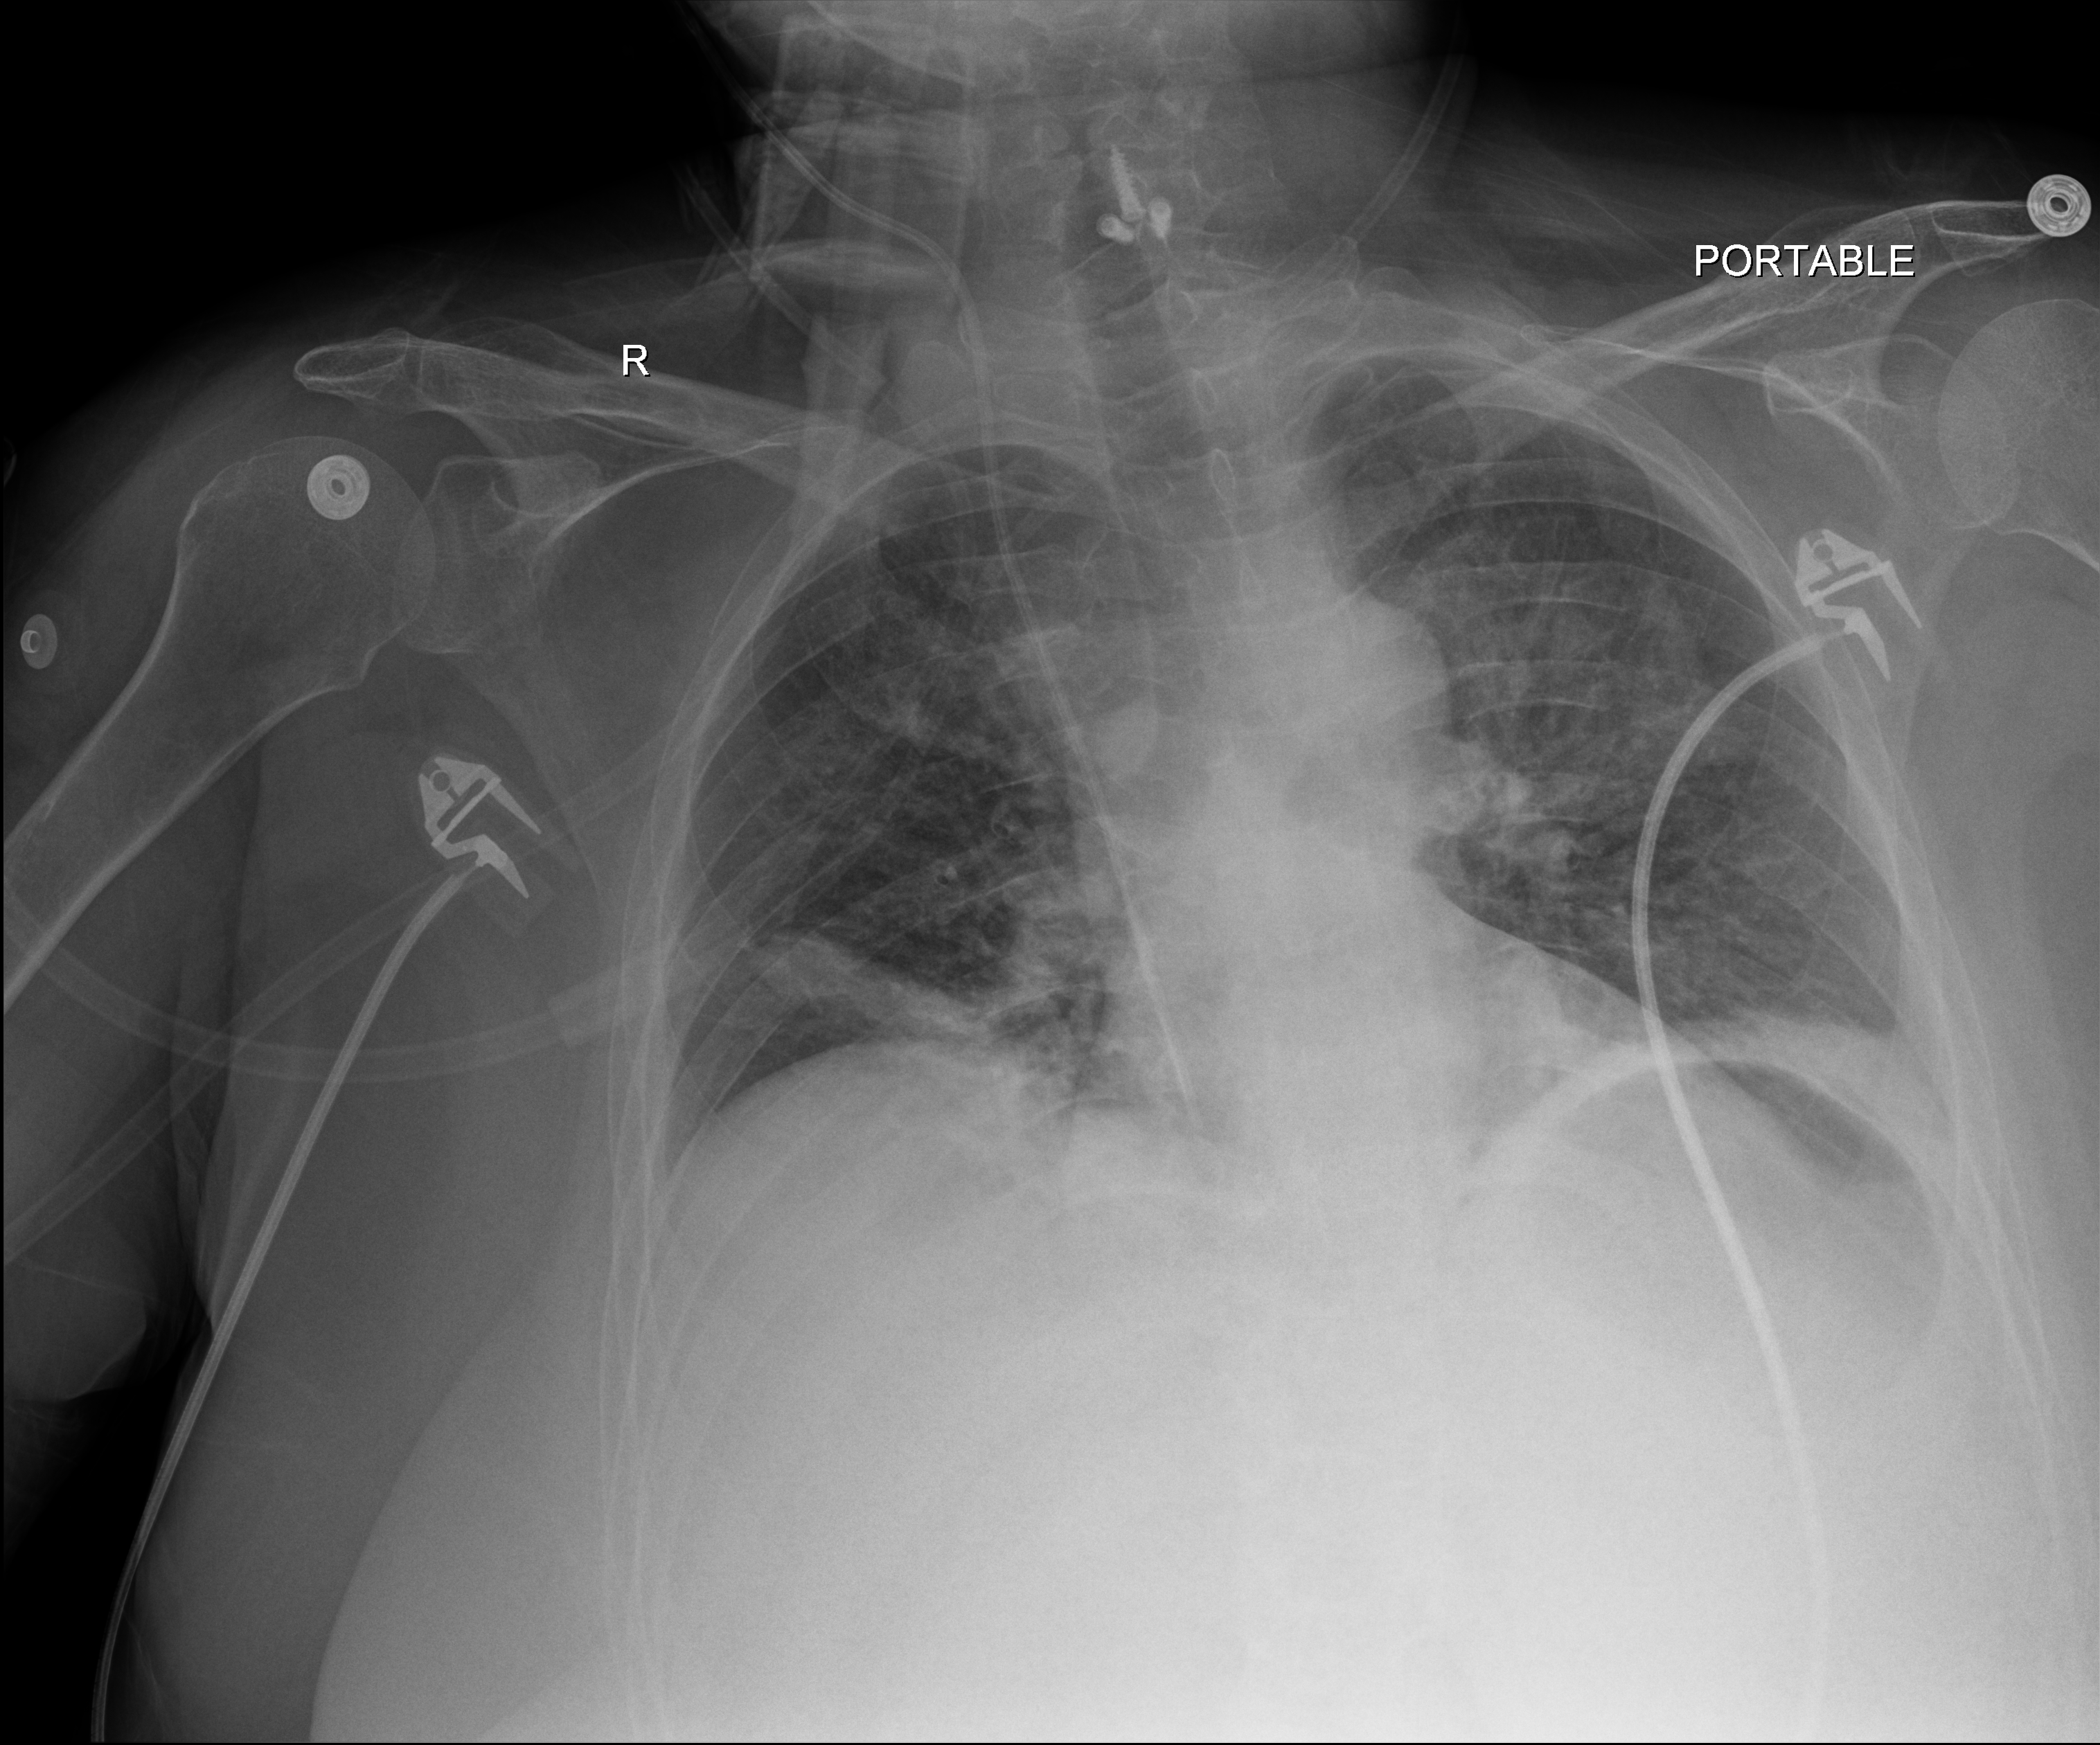
Chest X-ray (portable). Female patient hospitalised with COVID-19, age 18–59 years.
Hospital-stay facts (about this admission, not read from this image; timing relative to this image not recorded): admitted to intensive care during this hospital stay: yes; mechanically ventilated during this hospital stay: no; length of hospital stay: 44 days.